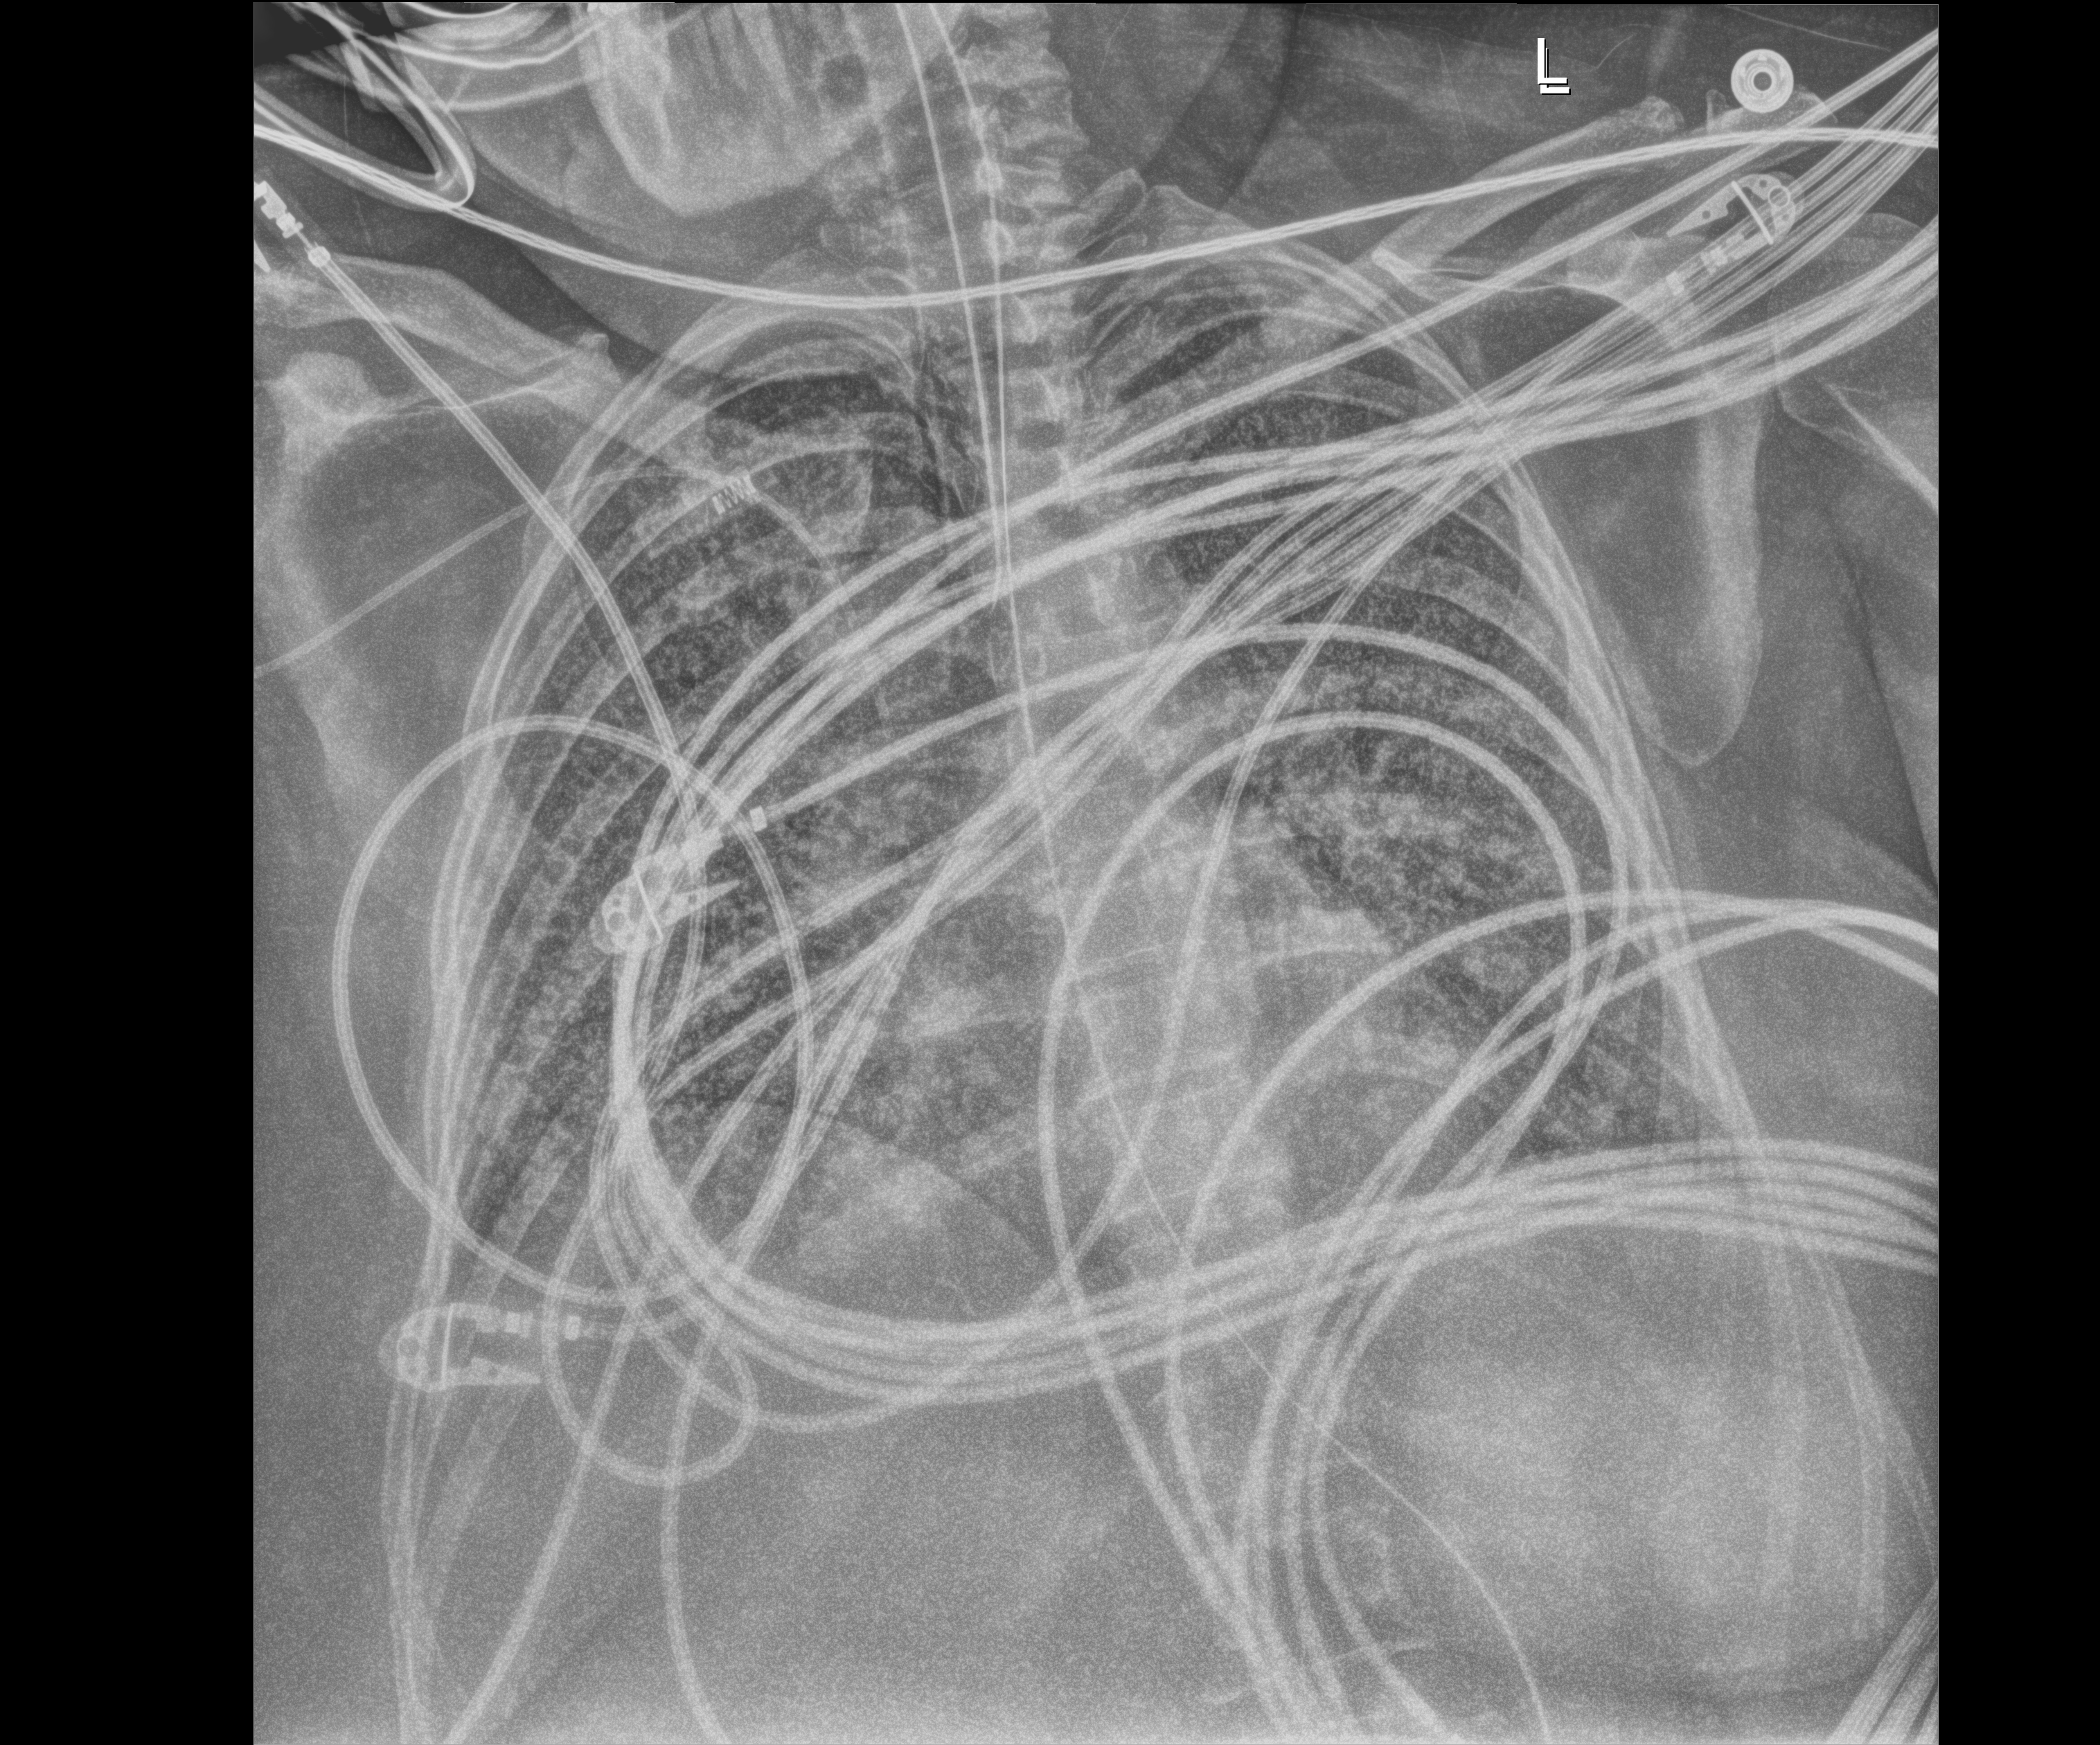
Chest X-ray (portable), anteroposterior (AP) projection. Patient hospitalised with COVID-19; female, aged 18–59 years.
Admission-level facts for this patient (not findings on this image; timing relative to this image not recorded):
- admitted to intensive care during this hospital stay: yes
- mechanically ventilated during this hospital stay: yes
- length of hospital stay: 95 days